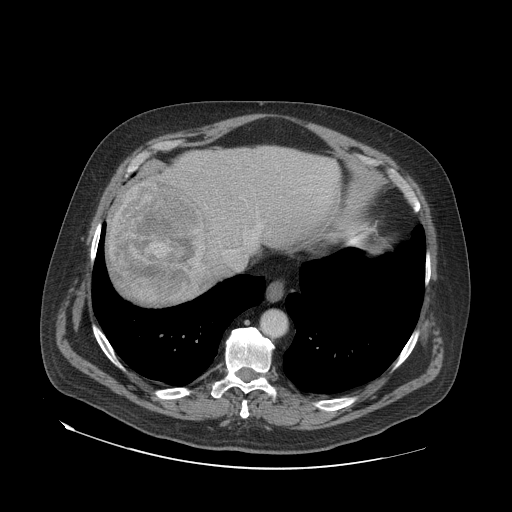
Contrast-enhanced abdominal CT (liver protocol), one axial slice. Slice 63 of 79 in the series (ordered by position). Reconstruction kernel STANDARD. Soft-tissue window (W 400 / L 40 HU). 512 × 512 image matrix, field of view 480 × 480 mm. Case-level facts recorded for this patient, not image findings: diagnosis: hepatocellular carcinoma (patient treated with transarterial chemoembolisation; whether this scan precedes or follows treatment is not stated here); TNM stage (as recorded): Stage-IVA; Child-Pugh class: A; tumour differentiation: well differentiated; tumour nodularity: multinodular.
Annotated regions visible in this slice (semi-automatic segmentation, software-assisted and operator-edited):
- abdominal aorta: box from (x=261, y=312) to (x=286, y=336) px
- liver parenchyma outside the tumour (the mass and vessels are separate outlines, so this box may not span the whole liver): (x=106, y=146)–(x=346, y=304)
- mass: (x=111, y=180)–(x=207, y=301)